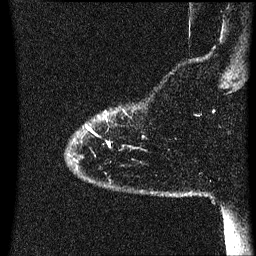
Breast MRI (dynamic contrast-enhanced), one sagittal slice. Slice 6 of 60 in the series (ordered by position). Dynamic contrast-enhanced series, image 2 of 3 at this slice position (ordered by acquisition). 1.5 T. TE 4.2 ms, TR 8.4 ms. 2.2 mm slice thickness. 256 × 256 image matrix. Patient: female, 35 years. Case-level facts recorded for this patient, not image findings: setting: breast cancer imaged before/during neoadjuvant chemotherapy; receptor status: HER2-positive.
Annotated regions visible in this slice (semi-automatically segmented with operator editing):
- analysis volume of interest (the breast-tissue region the enhancement analysis was run in; not a lesion): bounding box [x1, y1, x2, y2] px = [70, 112, 144, 169]
- tumour enhancement mask (voxels above the 70 % enhancement threshold inside the analysis volume of interest): [109, 144, 112, 147]